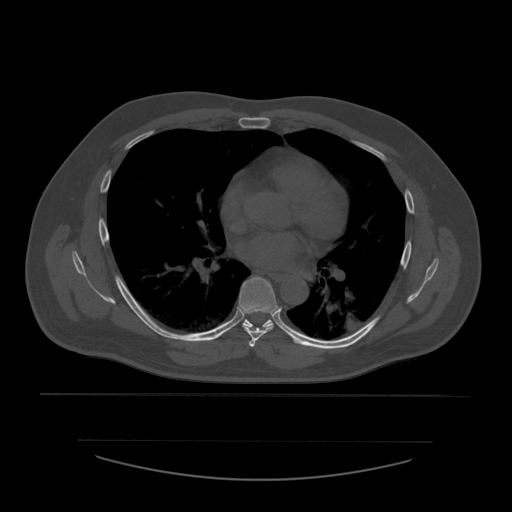
CT including the spine, one axial slice; slice 371 of 532 in the series (ordered by position); bone window (W 1800 / L 400 HU); 1.25 mm slice thickness; 512 × 512 image matrix, field of view 441 × 441 mm. Patient age 44 years. From the clinical record (not read from this slice): primary cancer: soft tissue sarcoma.
Annotated regions visible in this slice (semi-automatic segmentation, software-assisted and operator-edited):
- T5 vertebra: bounding box [x1, y1, x2, y2] px = [249, 341, 255, 348]
- T6 vertebra: [239, 277, 278, 344]
- T7 vertebra: [243, 320, 274, 328]